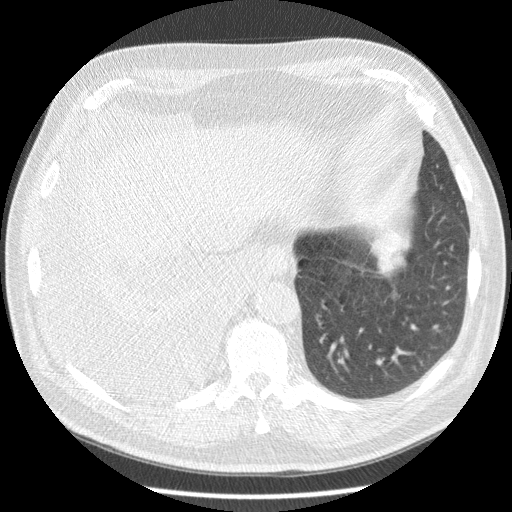
Axial slice from a low-dose chest CT screening exam; third annual screen; lung window (W 1500 / L -600 HU); 2.5 mm slice thickness; slice 51 of 180 in the series; 512 × 512 image matrix, field of view 355 × 355 mm. Male participant, aged 63 years at enrolment.
Expert reader's lesion annotation, bounding box (x1, y1, x2, y2) in pixels: (359, 215, 422, 280). Reader record for this screening exam (exam-level; its link to the box is not recorded): non-calcified nodule or mass ≥4 mm, left lower lobe, 34 × 31 mm, smooth margins, soft tissue attenuation, pre-existing on the prior screen: yes; interval growth: yes.